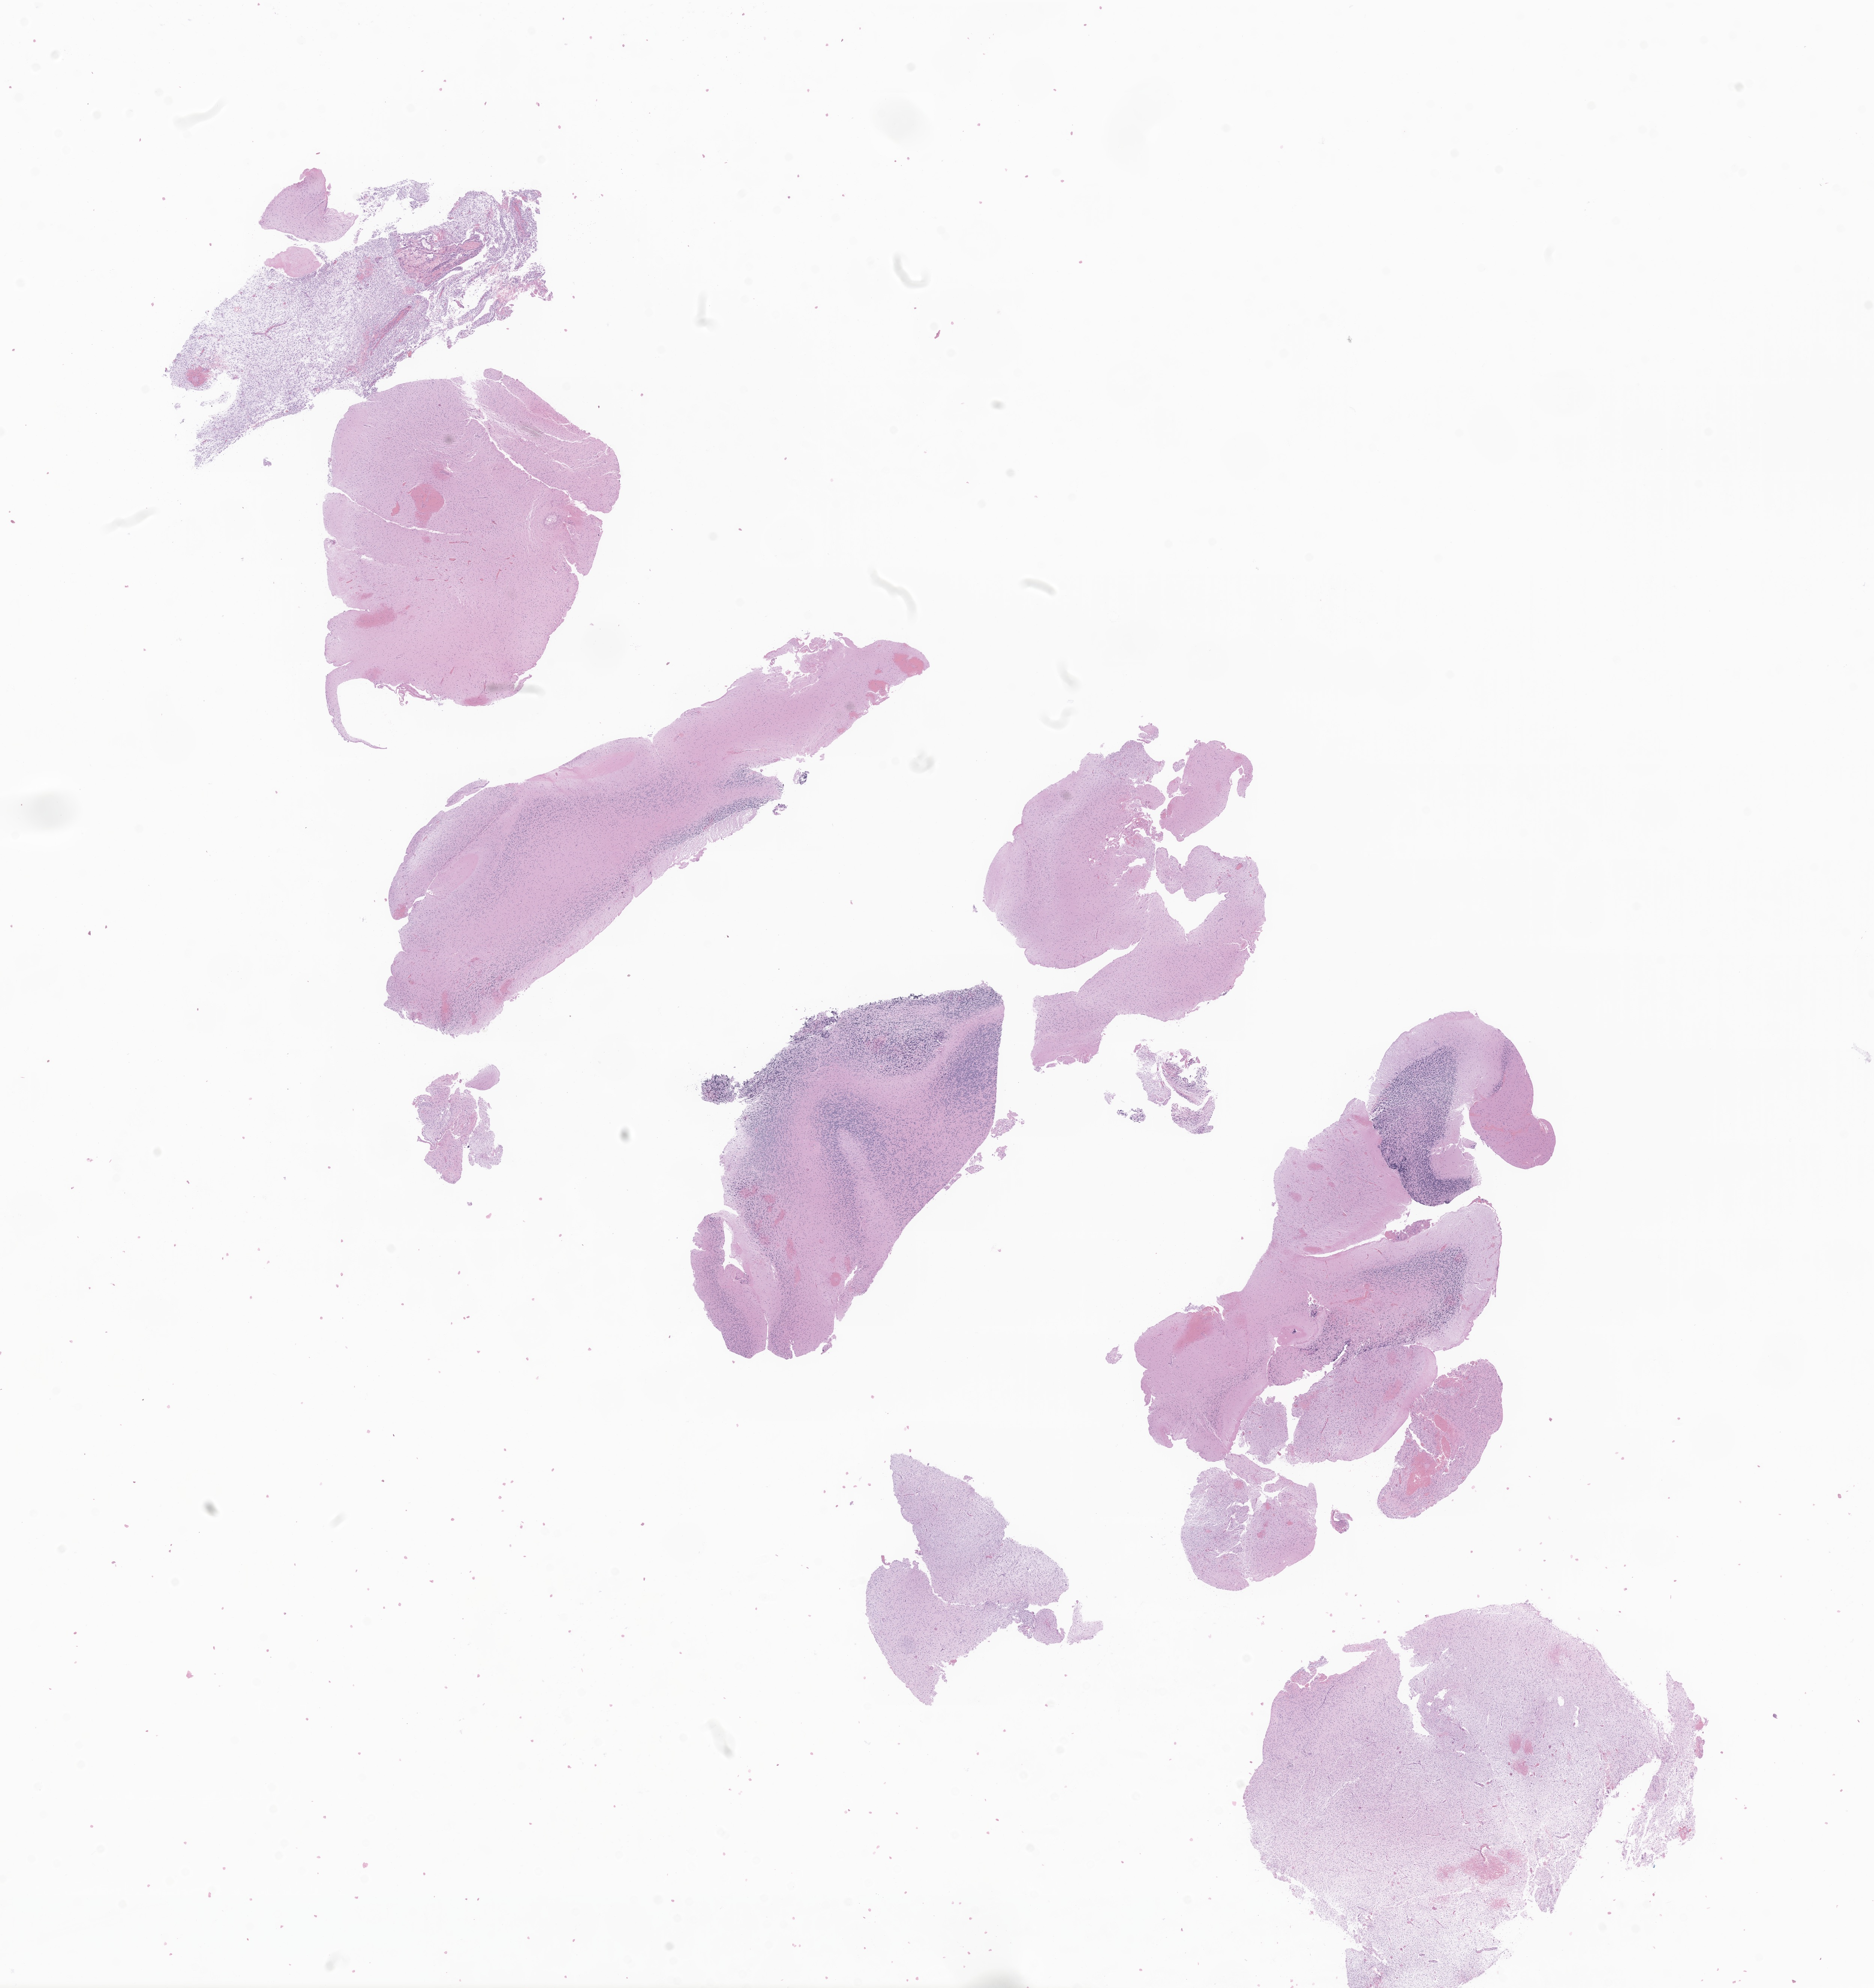
Whole-slide image, haematoxylin and eosin stain of tumor tissue from the brain — whole scanned area (about 21.1 x 22.4 mm) shown as a low-resolution overview; formalin-fixed, paraffin-embedded (FFPE) tissue. Patient: male, age 822 days.
Diagnosis (ICD-O-3 morphology term): Neoplasm, malignant.